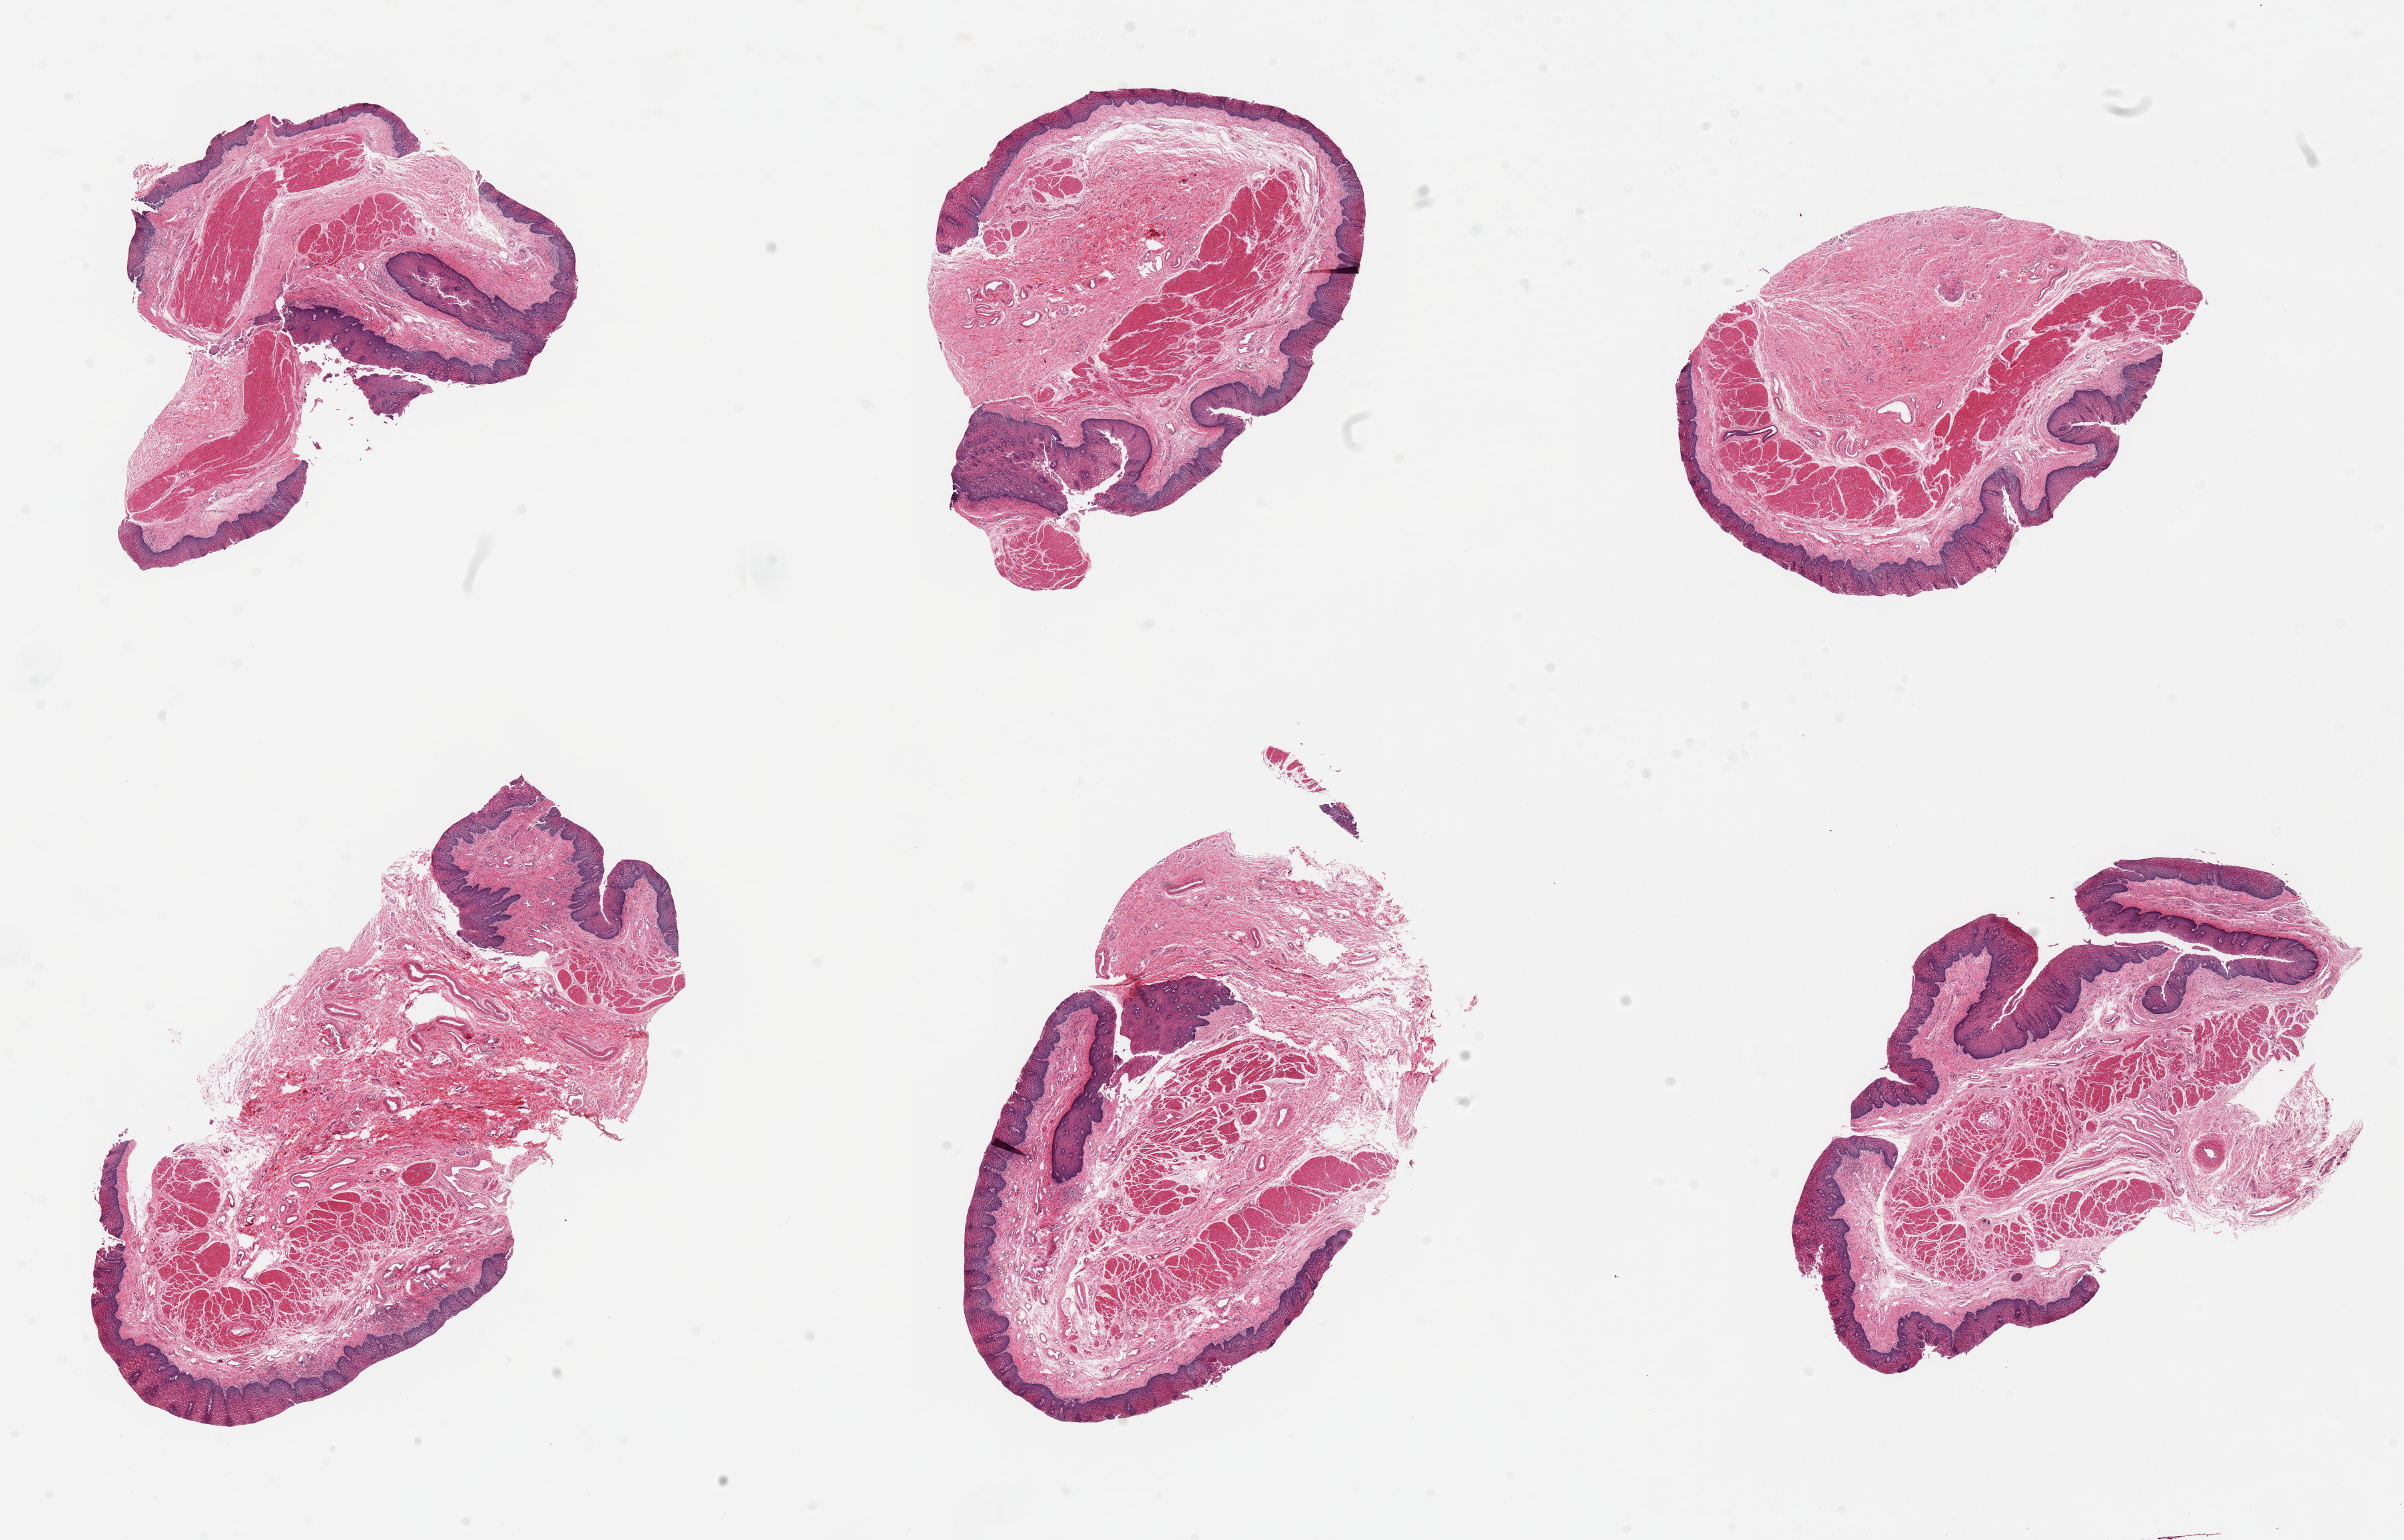
Whole-slide image, haematoxylin and eosin stain, a low-resolution overview of the entire scanned area, about 28.5 x 18.3 mm. PAXgene-fixed, paraffin-embedded tissue. Sampled site (target tissue): esophageal mucous membrane. Tissue donor sample. Donor sex: male.
• pathologist's review note for this sample: 6 pieces; squamous mucosa is ~0.5mm, ~10% thickness